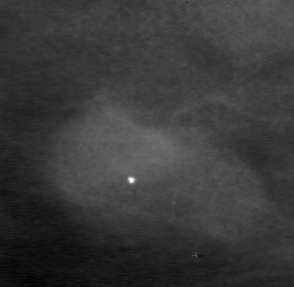
Crop from a digitized film mammogram around one marked abnormality, left breast, CC view.
- Marked abnormality: mass, shape lobulated, margins circumscribed; BI-RADS assessment category 4; subtlety rating 3 on a 1 (subtle) to 5 (obvious) scale; pathology (as recorded): benign.